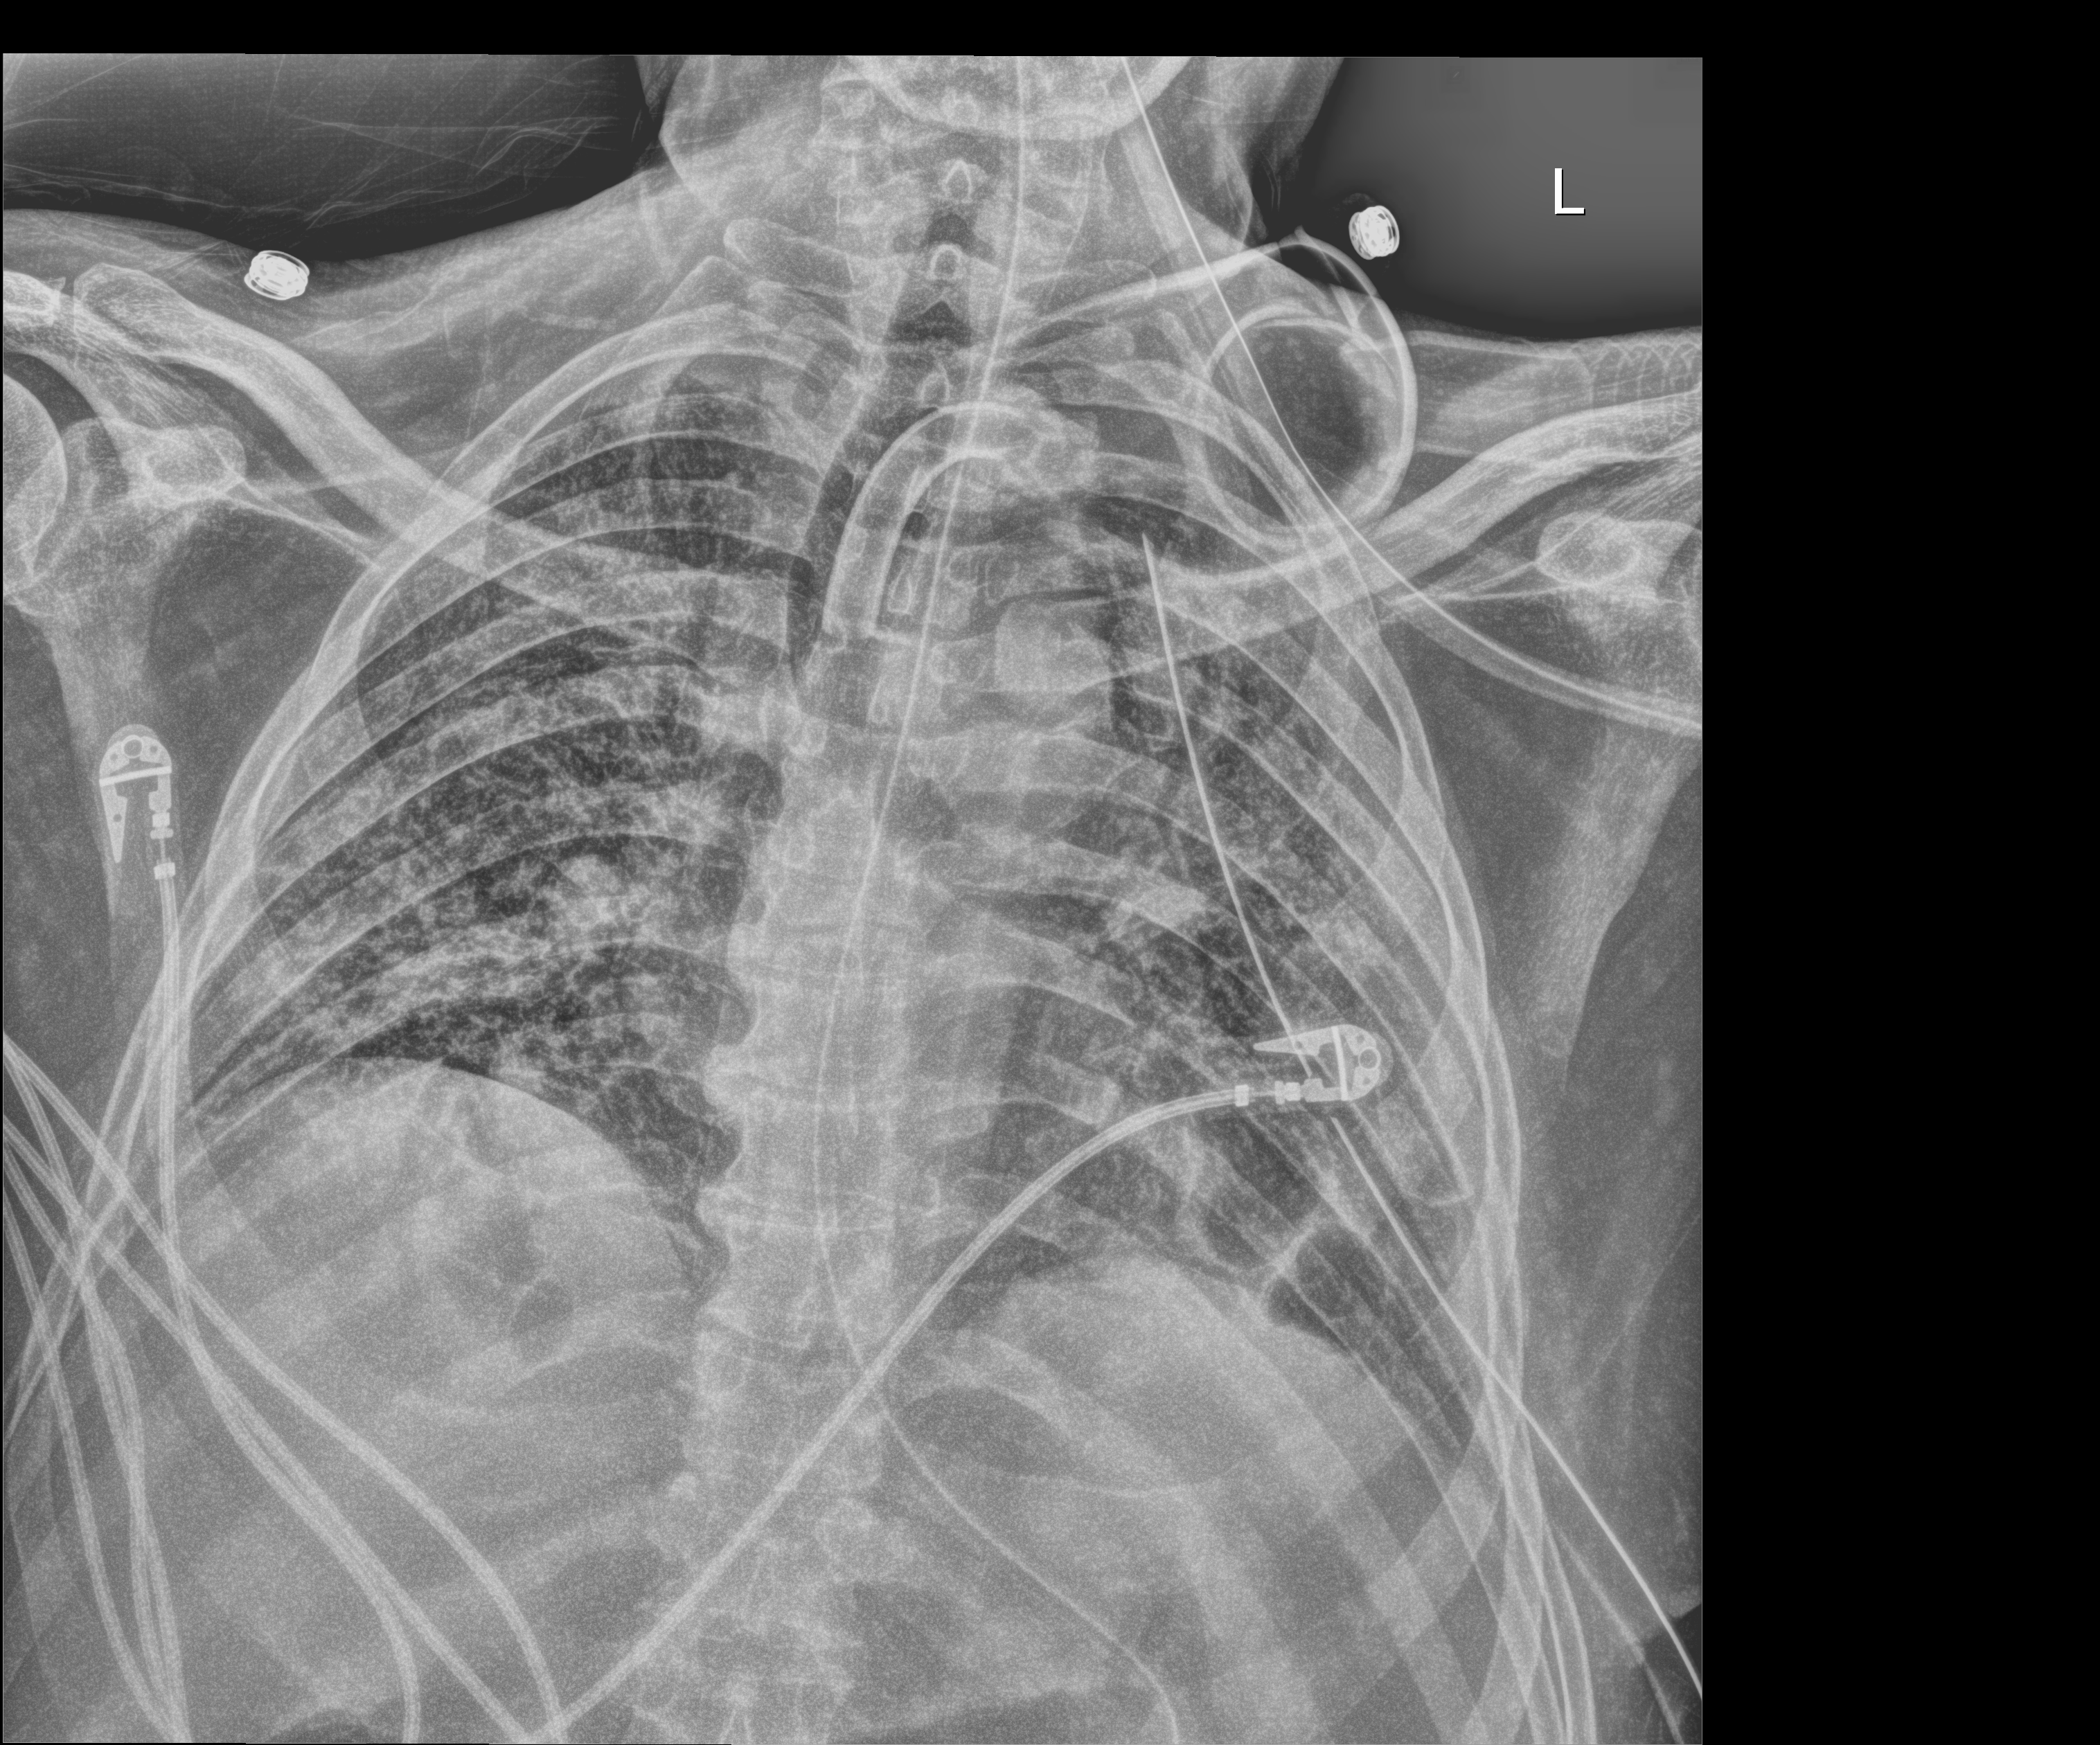
Portable chest radiograph, anteroposterior (AP) projection. Male patient hospitalised with COVID-19, age 18–59 years.
Admission-level facts for this patient (not findings on this image; timing relative to this image not recorded):
- admitted to intensive care during this hospital stay: yes
- length of hospital stay: 83 days